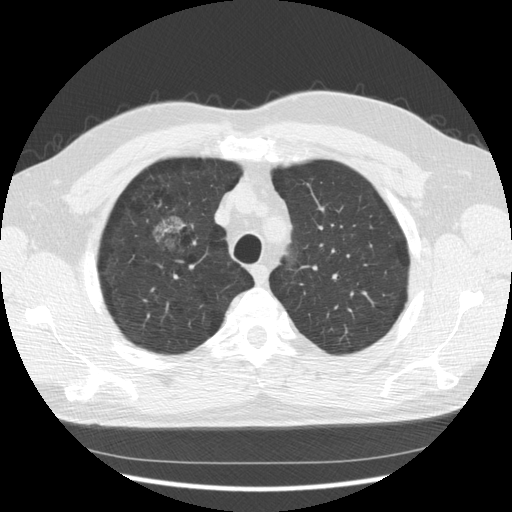
Low-dose screening chest CT, one axial slice. Position 99 of 133 along the scan axis. 140 kVp. Lung window (W 1500 / L -600 HU). 2.5 mm slice thickness. 512 × 512 image matrix, field of view 369 × 369 mm.
Structures marked on this image (outlined manually by an expert reader):
- lesion 1 (tumor, upper lobe of right lung): bounding box [x1, y1, x2, y2] px = [154, 218, 185, 241]